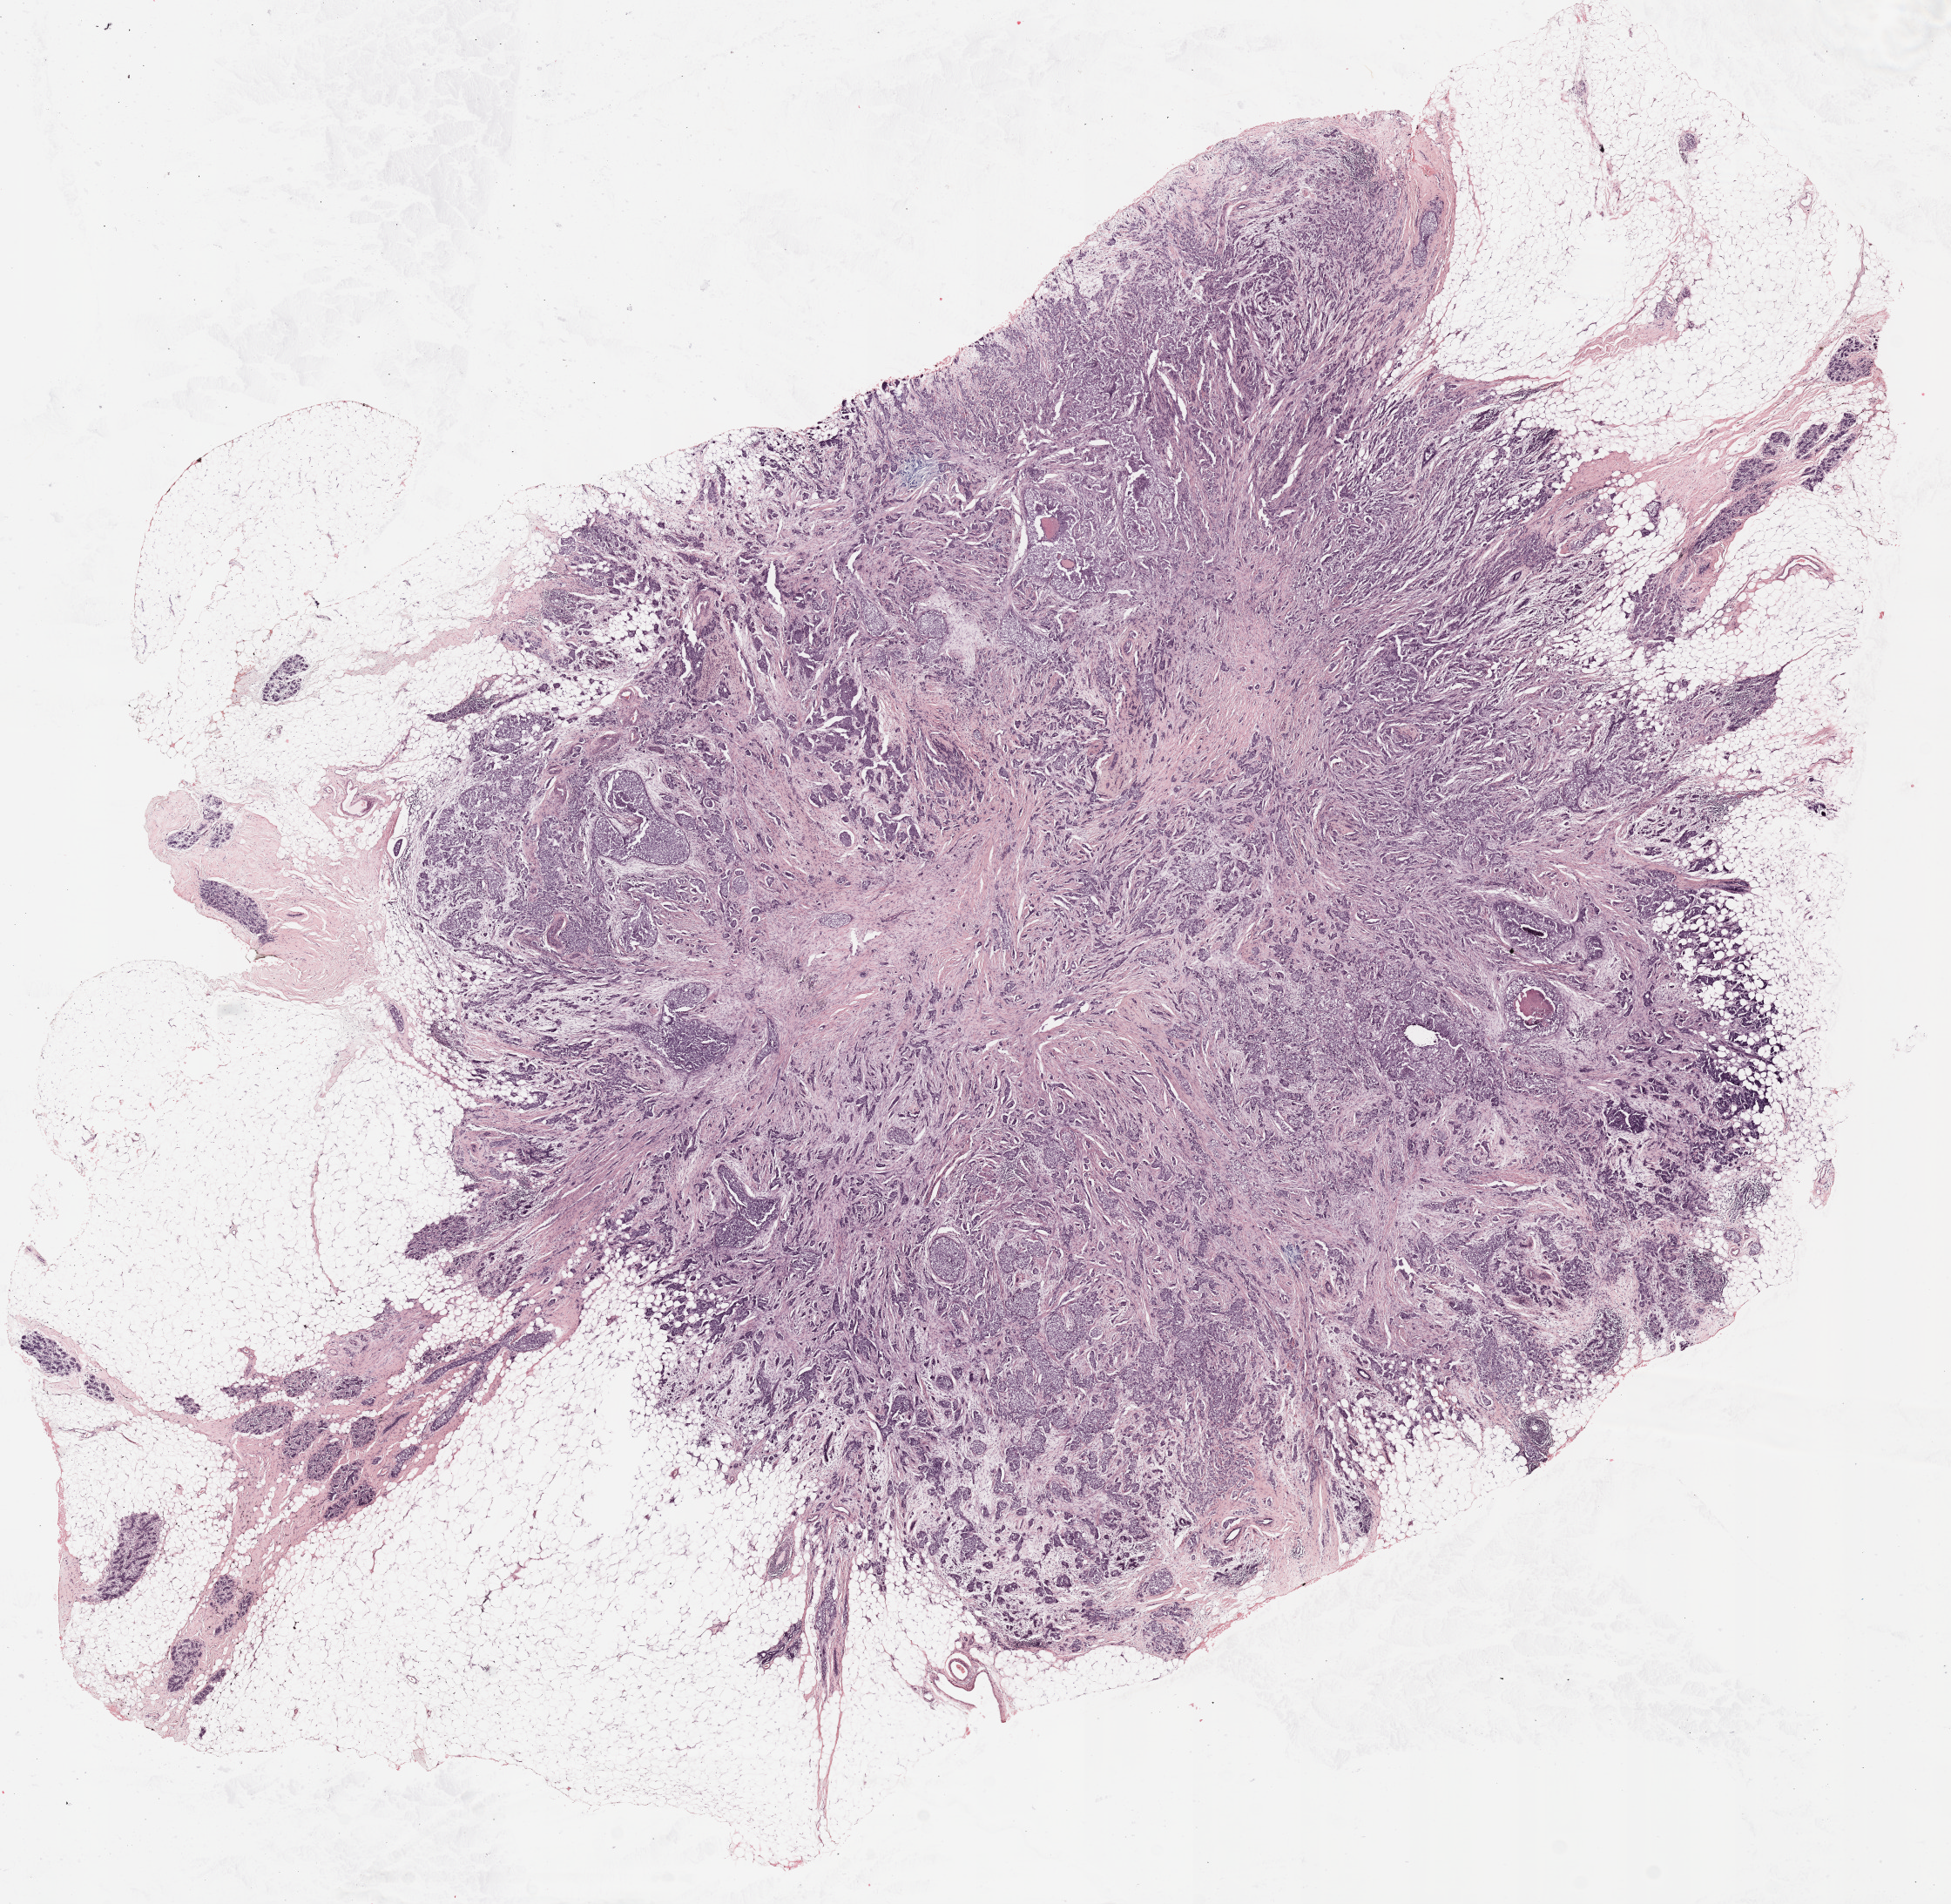
Whole-slide histology image, H&E, whole scanned area (about 17.9 x 17.5 mm) shown as a low-resolution overview. FFPE section. Breast, primary tumour sample. Female patient; age at initial diagnosis 41 years.
Diagnosis: Infiltrating duct carcinoma, NOS.